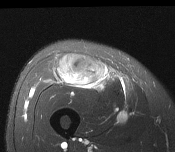
MRI of an extremity soft-tissue mass, one axial slice; slice 68 of 116 in the series (ordered by position); T2-weighted fat-saturated; MR volume resampled by the dataset authors to the PET/CT grid (not the native acquisition matrix); 3.27 mm slice thickness; 175 × 152 image matrix, field of view 171 × 148 mm. Male patient. Case-level facts recorded for this patient, not image findings: histological type: pleiomorphic leiomyosarcoma; grade: intermediate; site of the primary tumour: right thigh.
Structures marked on this image (expert contour drawn on MRI and transferred to this co-registered scan by the dataset authors):
- gross tumour volume including surrounding oedema: bounding box <56,54,107,89> (left, top, right, bottom; pixels)
- gross tumour volume (mass): <70,63,91,84>